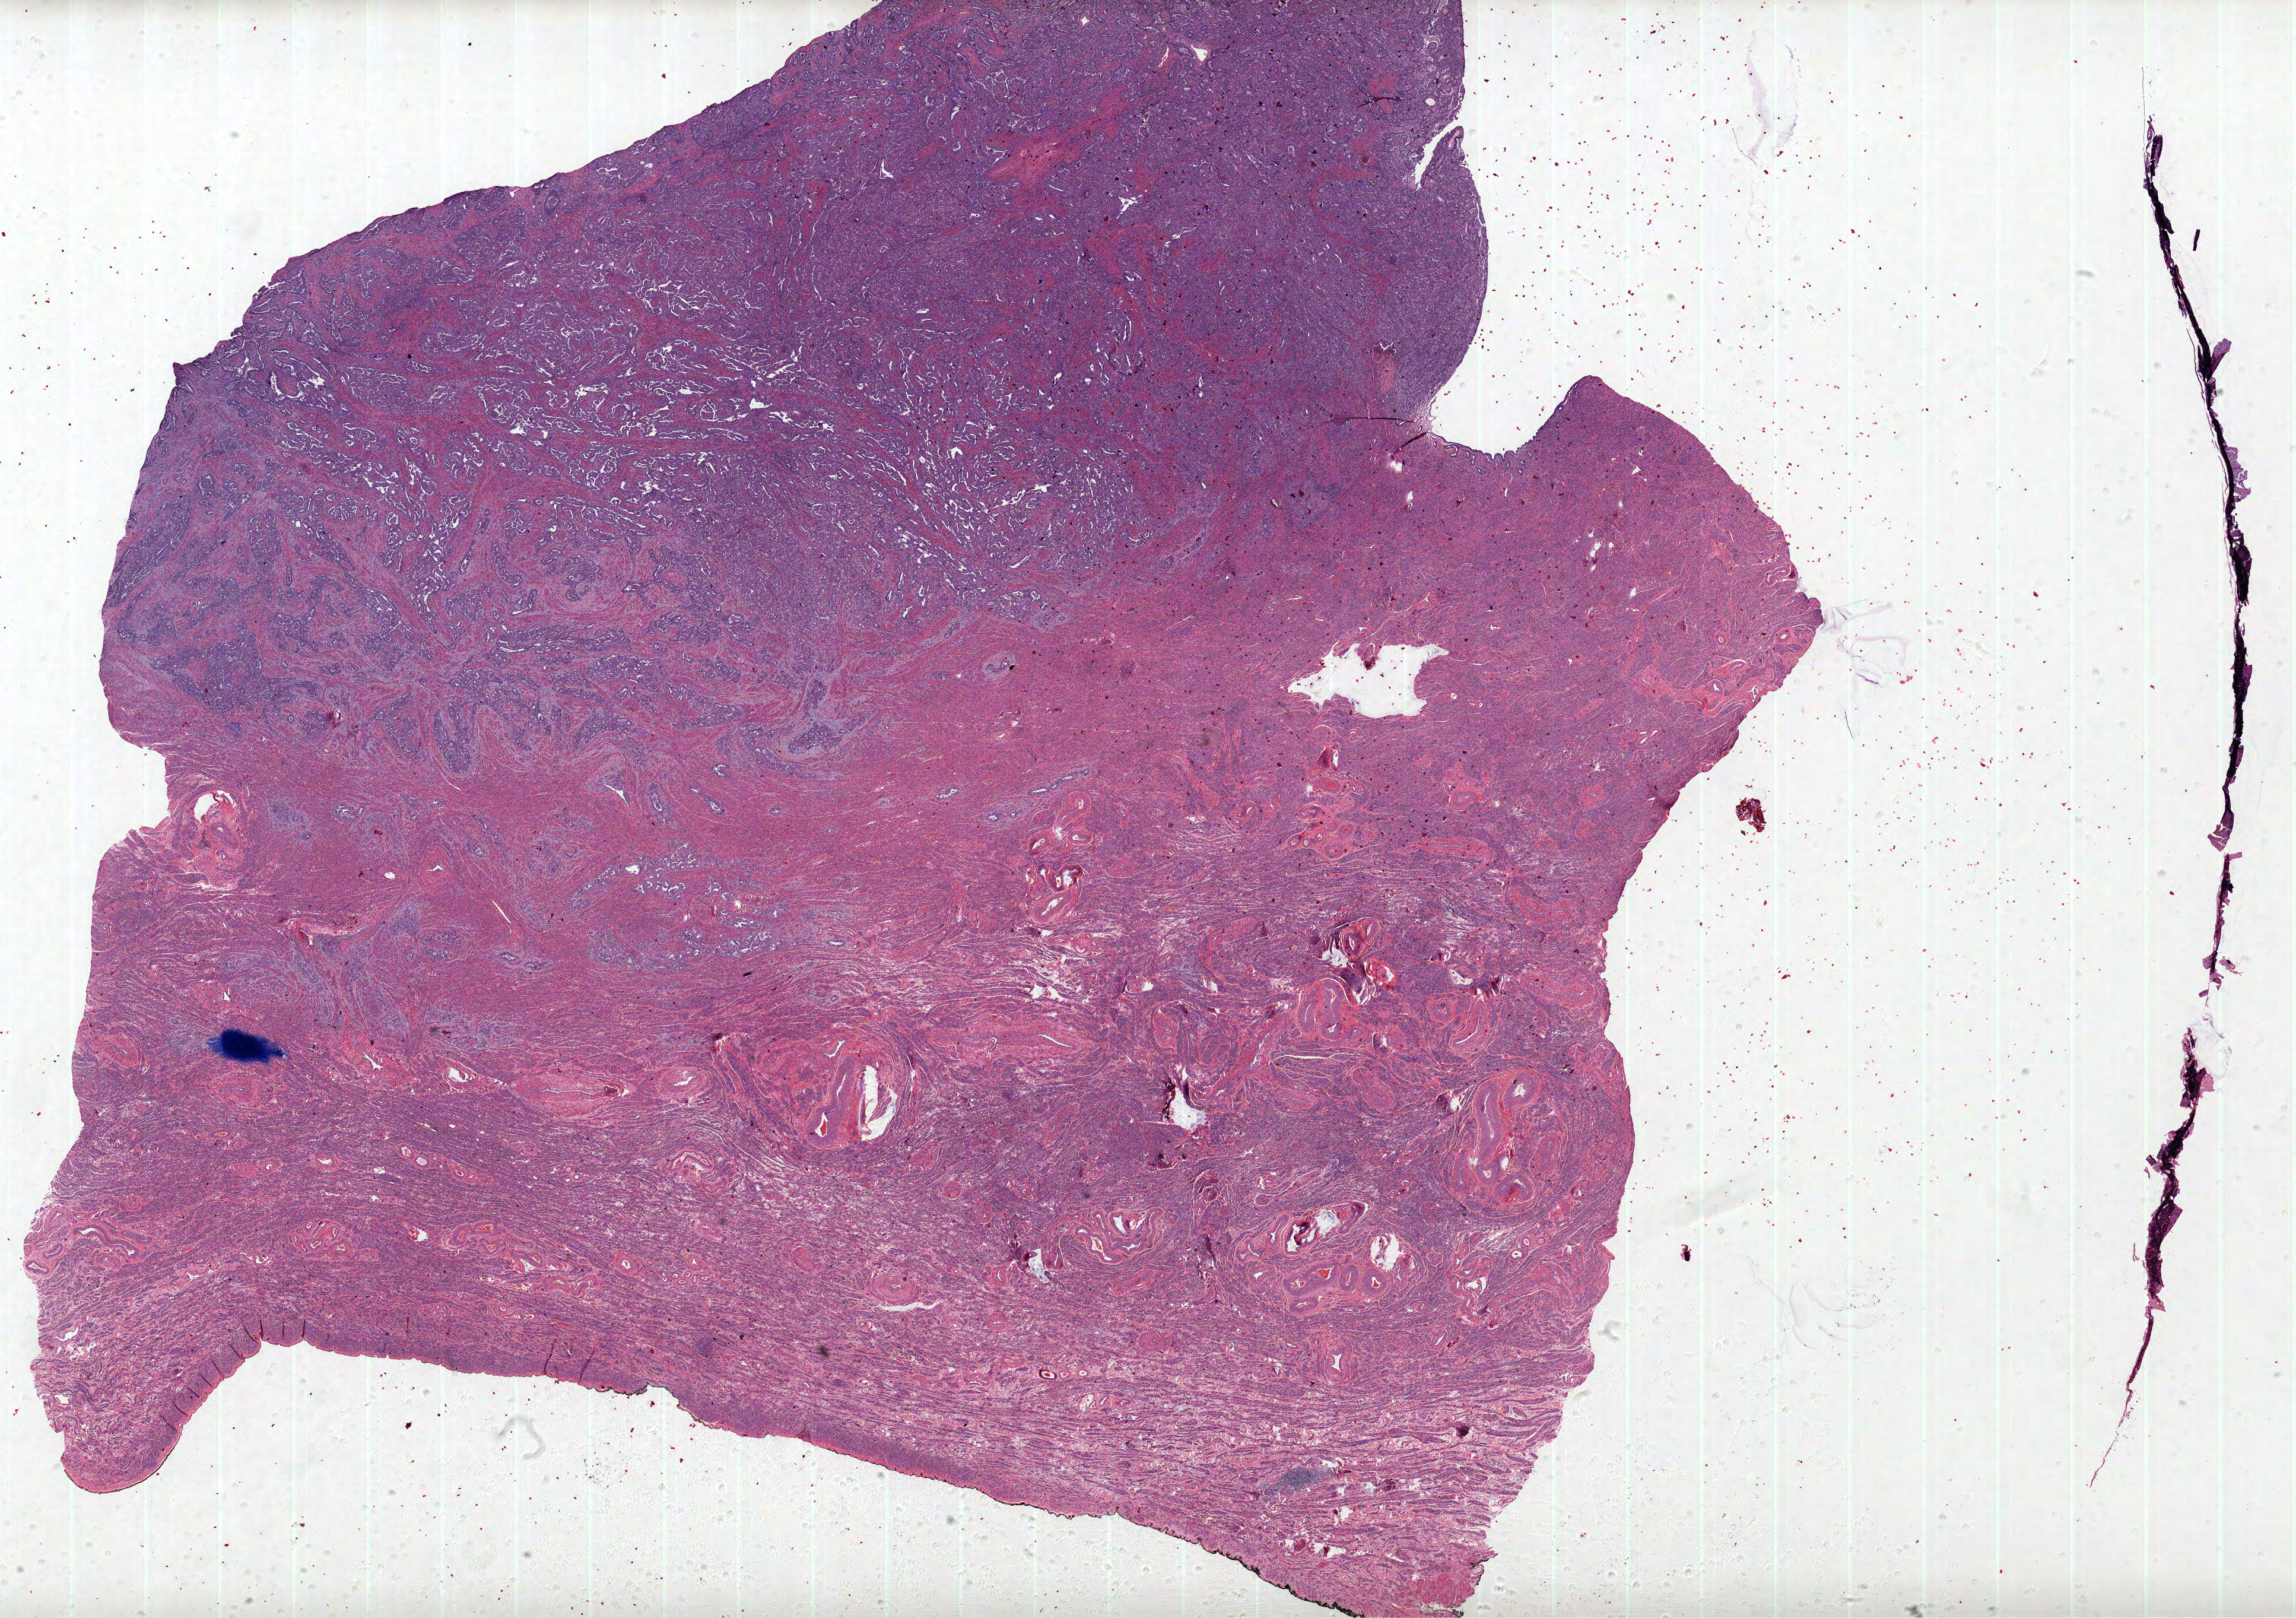
Hematoxylin and eosin (H&E) stained whole-slide image, whole scanned area (about 30.8 x 21.7 mm) shown as a low-resolution overview. Formalin-fixed paraffin-embedded (FFPE) diagnostic section. Primary tumour sample from the uterus. Female patient; age at initial diagnosis 67 years. Histologic grade: G3 (poorly differentiated).
Histologic diagnosis: Serous cystadenocarcinoma, NOS (endometrium). FIGO stage: IIIC2. Lymph nodes positive (case pathology): 1 of 29 examined.